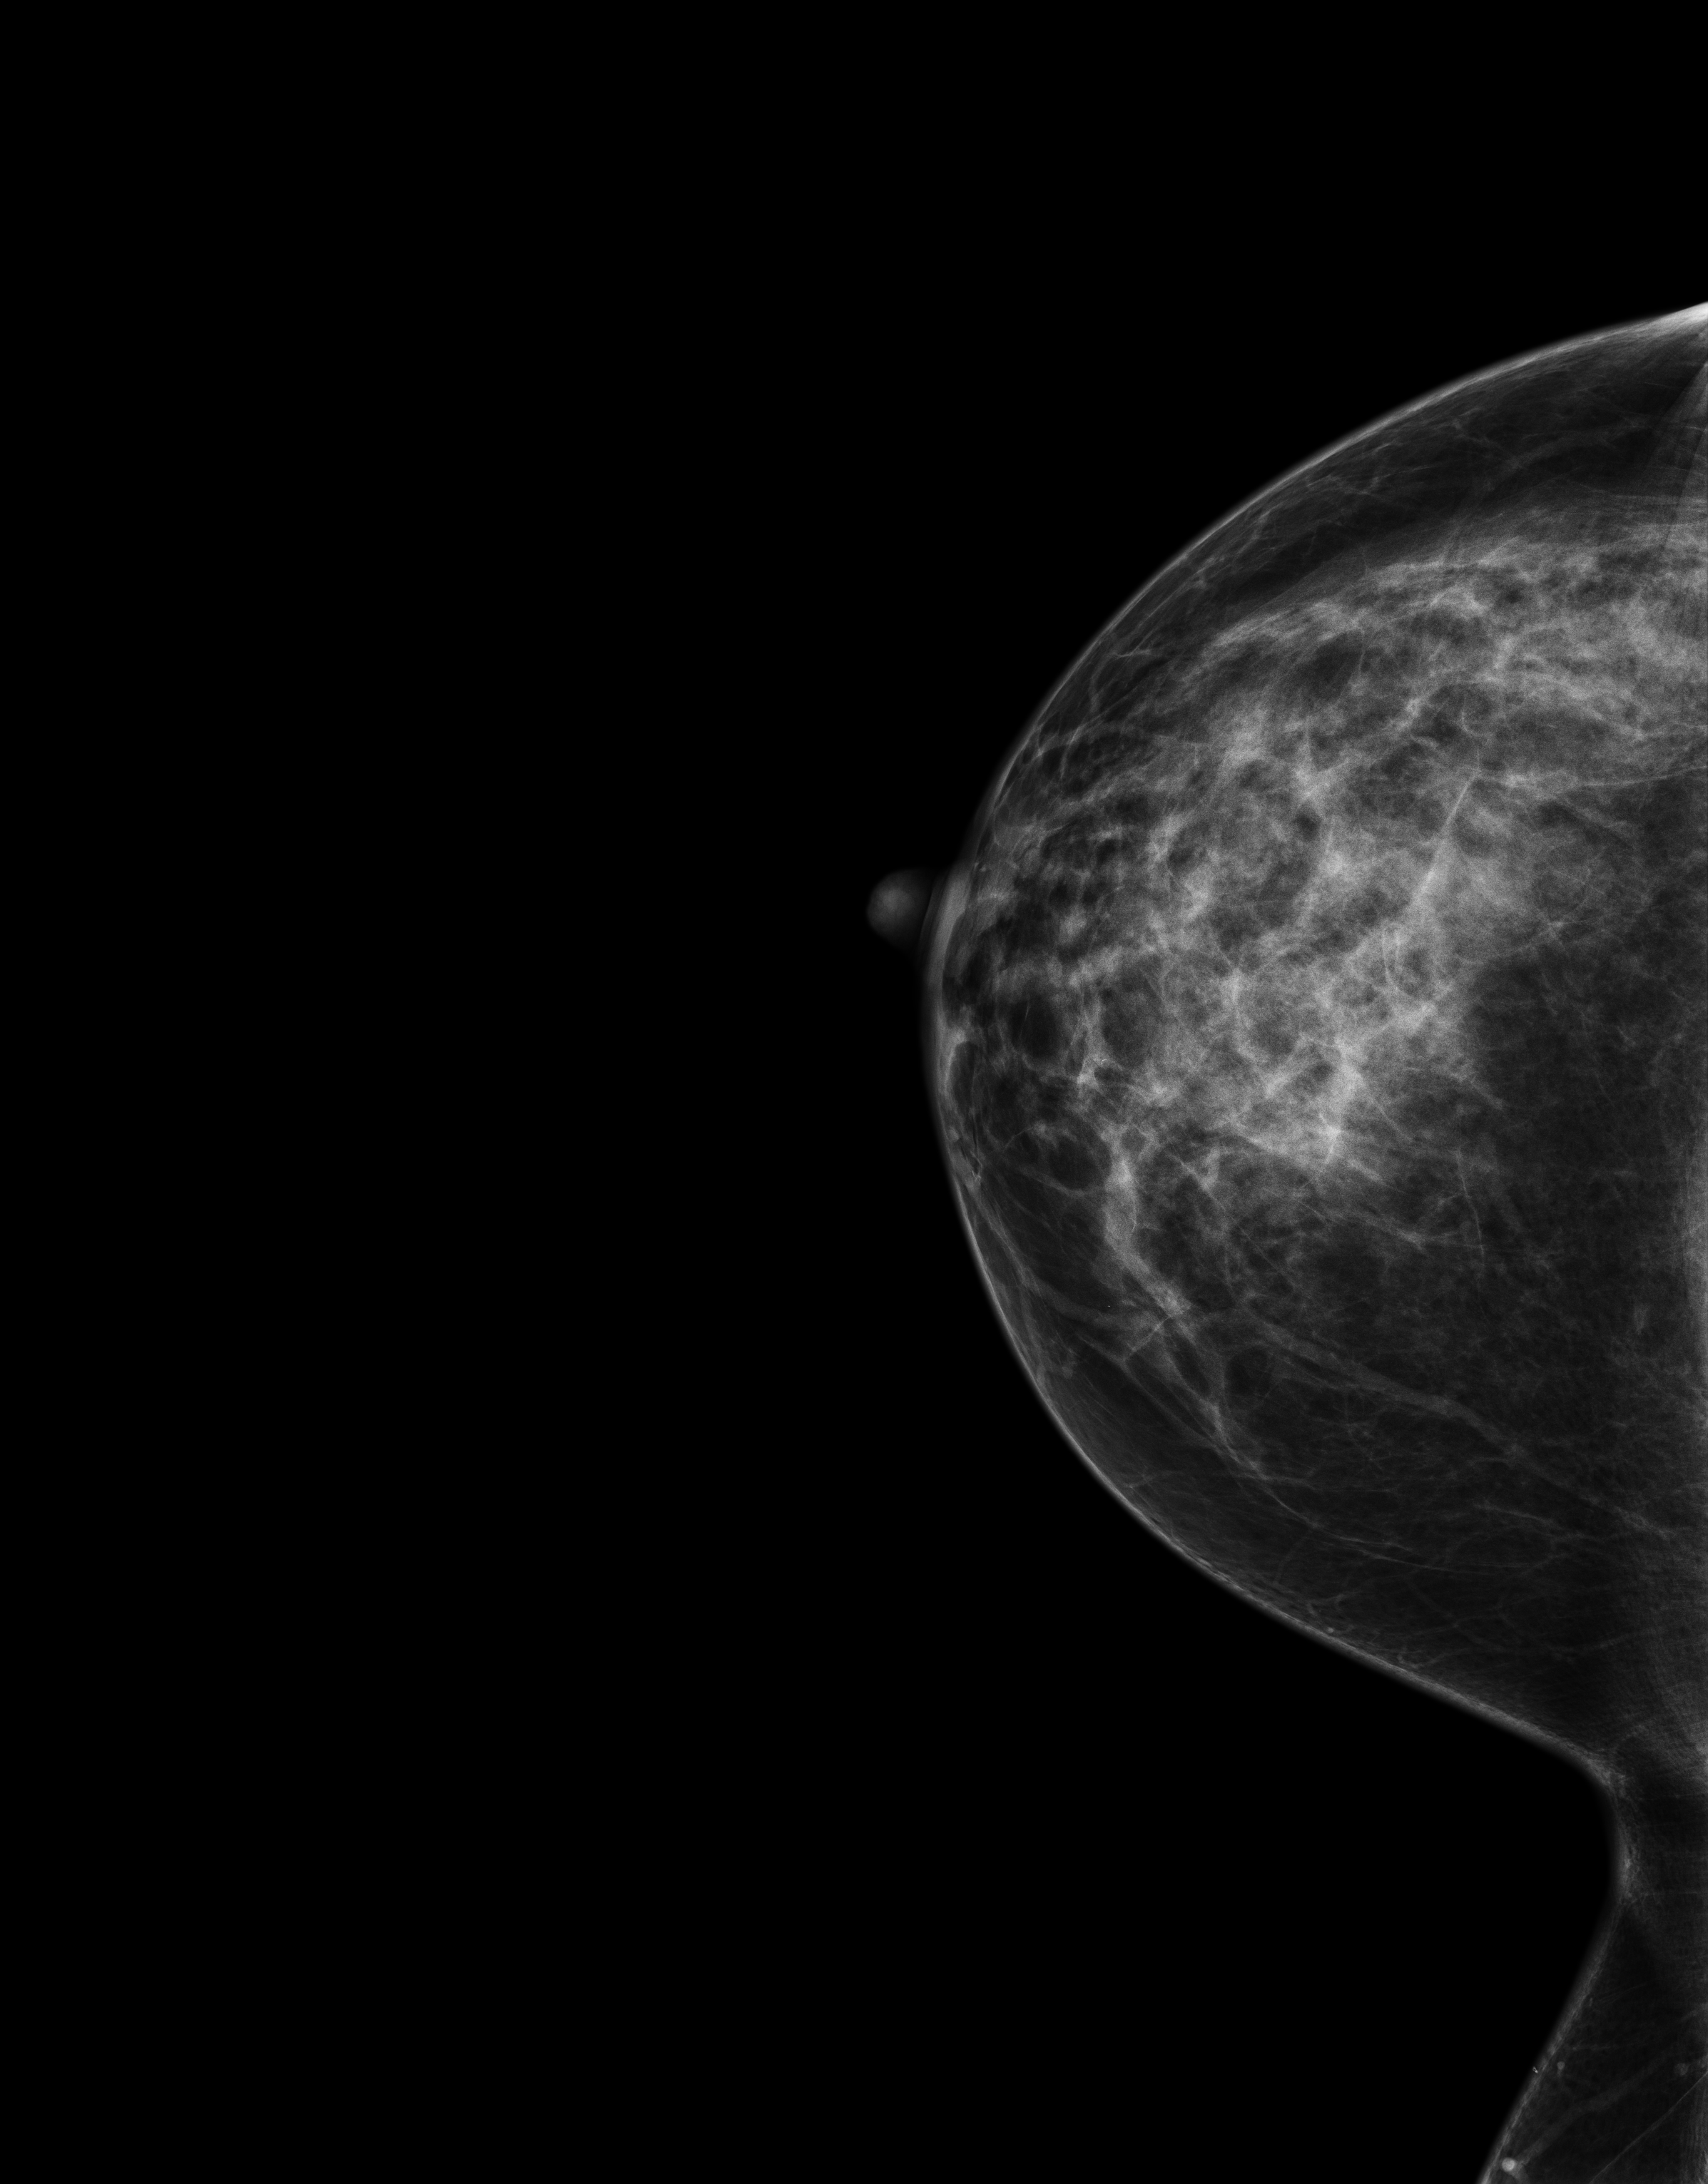
Annual screening mammography examination; compressed breast thickness 65 mm. Patient aged 50 years (female).
Image type: full-field digital mammogram. Breast: right. Projection: CC view.